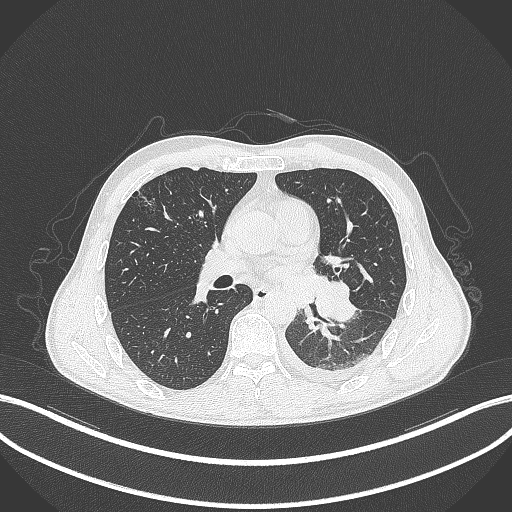
Chest CT, one axial slice. Slice 168 of 295 in the series (ordered by position). Lung window (W 1500 / L -600 HU). 512 × 512 image matrix, field of view 400 × 400 mm. Male patient, age 47 years. From the clinical record (not read from this slice): clinical TNM (as recorded): T3 N1 M1c; histopathological grade: G3.
Annotated regions visible in this slice (bounding box drawn by a radiologist):
- lung tumour (recorded histology: small cell carcinoma): bounding box <310,278,359,322> (left, top, right, bottom; pixels)